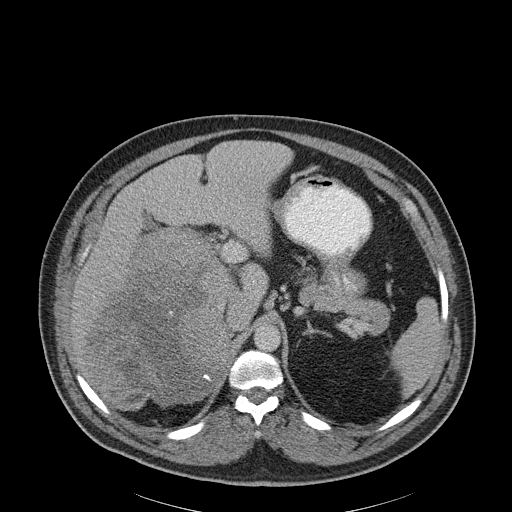
Contrast-enhanced abdominal CT, one axial slice. Position 139 of 186 along the scan axis. Reconstruction kernel B30f. 120 kVp. Soft-tissue window (W 400 / L 40 HU). 3 mm slice thickness. 512 × 512 image matrix, field of view 464 × 464 mm. Patient: male, 56 years. From the clinical record (not read from this slice): diagnosis: adrenocortical carcinoma; tumour side: right adrenal; tumour size at pathology: 18 cm; Ki-67 index: 2 %; stage (as recorded): 3.
Outlined on this slice (semi-automatically segmented with operator editing):
- mass: box from (x=84, y=230) to (x=227, y=405) px